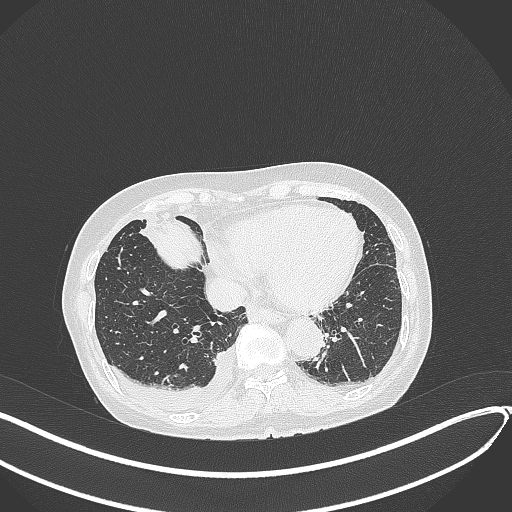
Chest CT, one axial slice. Slice 110 of 418 in the series (ordered by position). Reconstruction kernel B70f. Lung window (W 1500 / L -600 HU). 1 mm slice thickness. 512 × 512 image matrix, field of view 400 × 400 mm. Patient: female, 75 years. From the clinical record (not read from this slice): clinical TNM (as recorded): T2a N3 M0.
Structures marked on this image (bounding box drawn by a radiologist):
- lung tumour (recorded histology: adenocarcinoma): bounding box (x1, y1, x2, y2) in pixels: (142, 218, 201, 271)